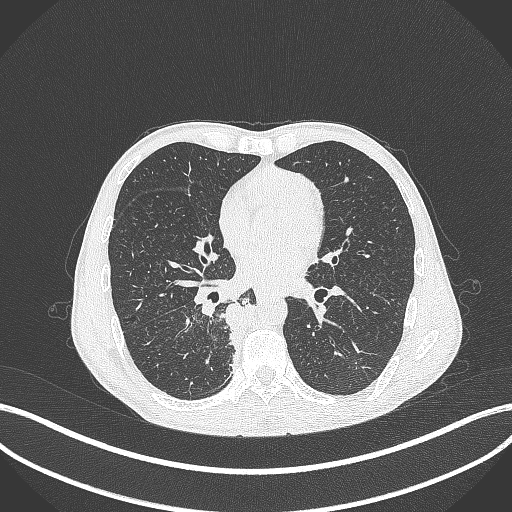
Chest CT, one axial slice. Slice 177 of 371 in the series (ordered by position). Reconstruction kernel B70f. 120 kVp. Lung window (W 1500 / L -600 HU). 1 mm slice thickness. 512 × 512 image matrix. Male patient, age 58 years. Case-level facts recorded for this patient, not image findings: clinical TNM (as recorded): T3 N1 M1.
Annotated regions visible in this slice (rectangle marked by the reading radiologist):
- lung tumour (recorded histology: squamous cell carcinoma): box from (x=217, y=295) to (x=258, y=363) px